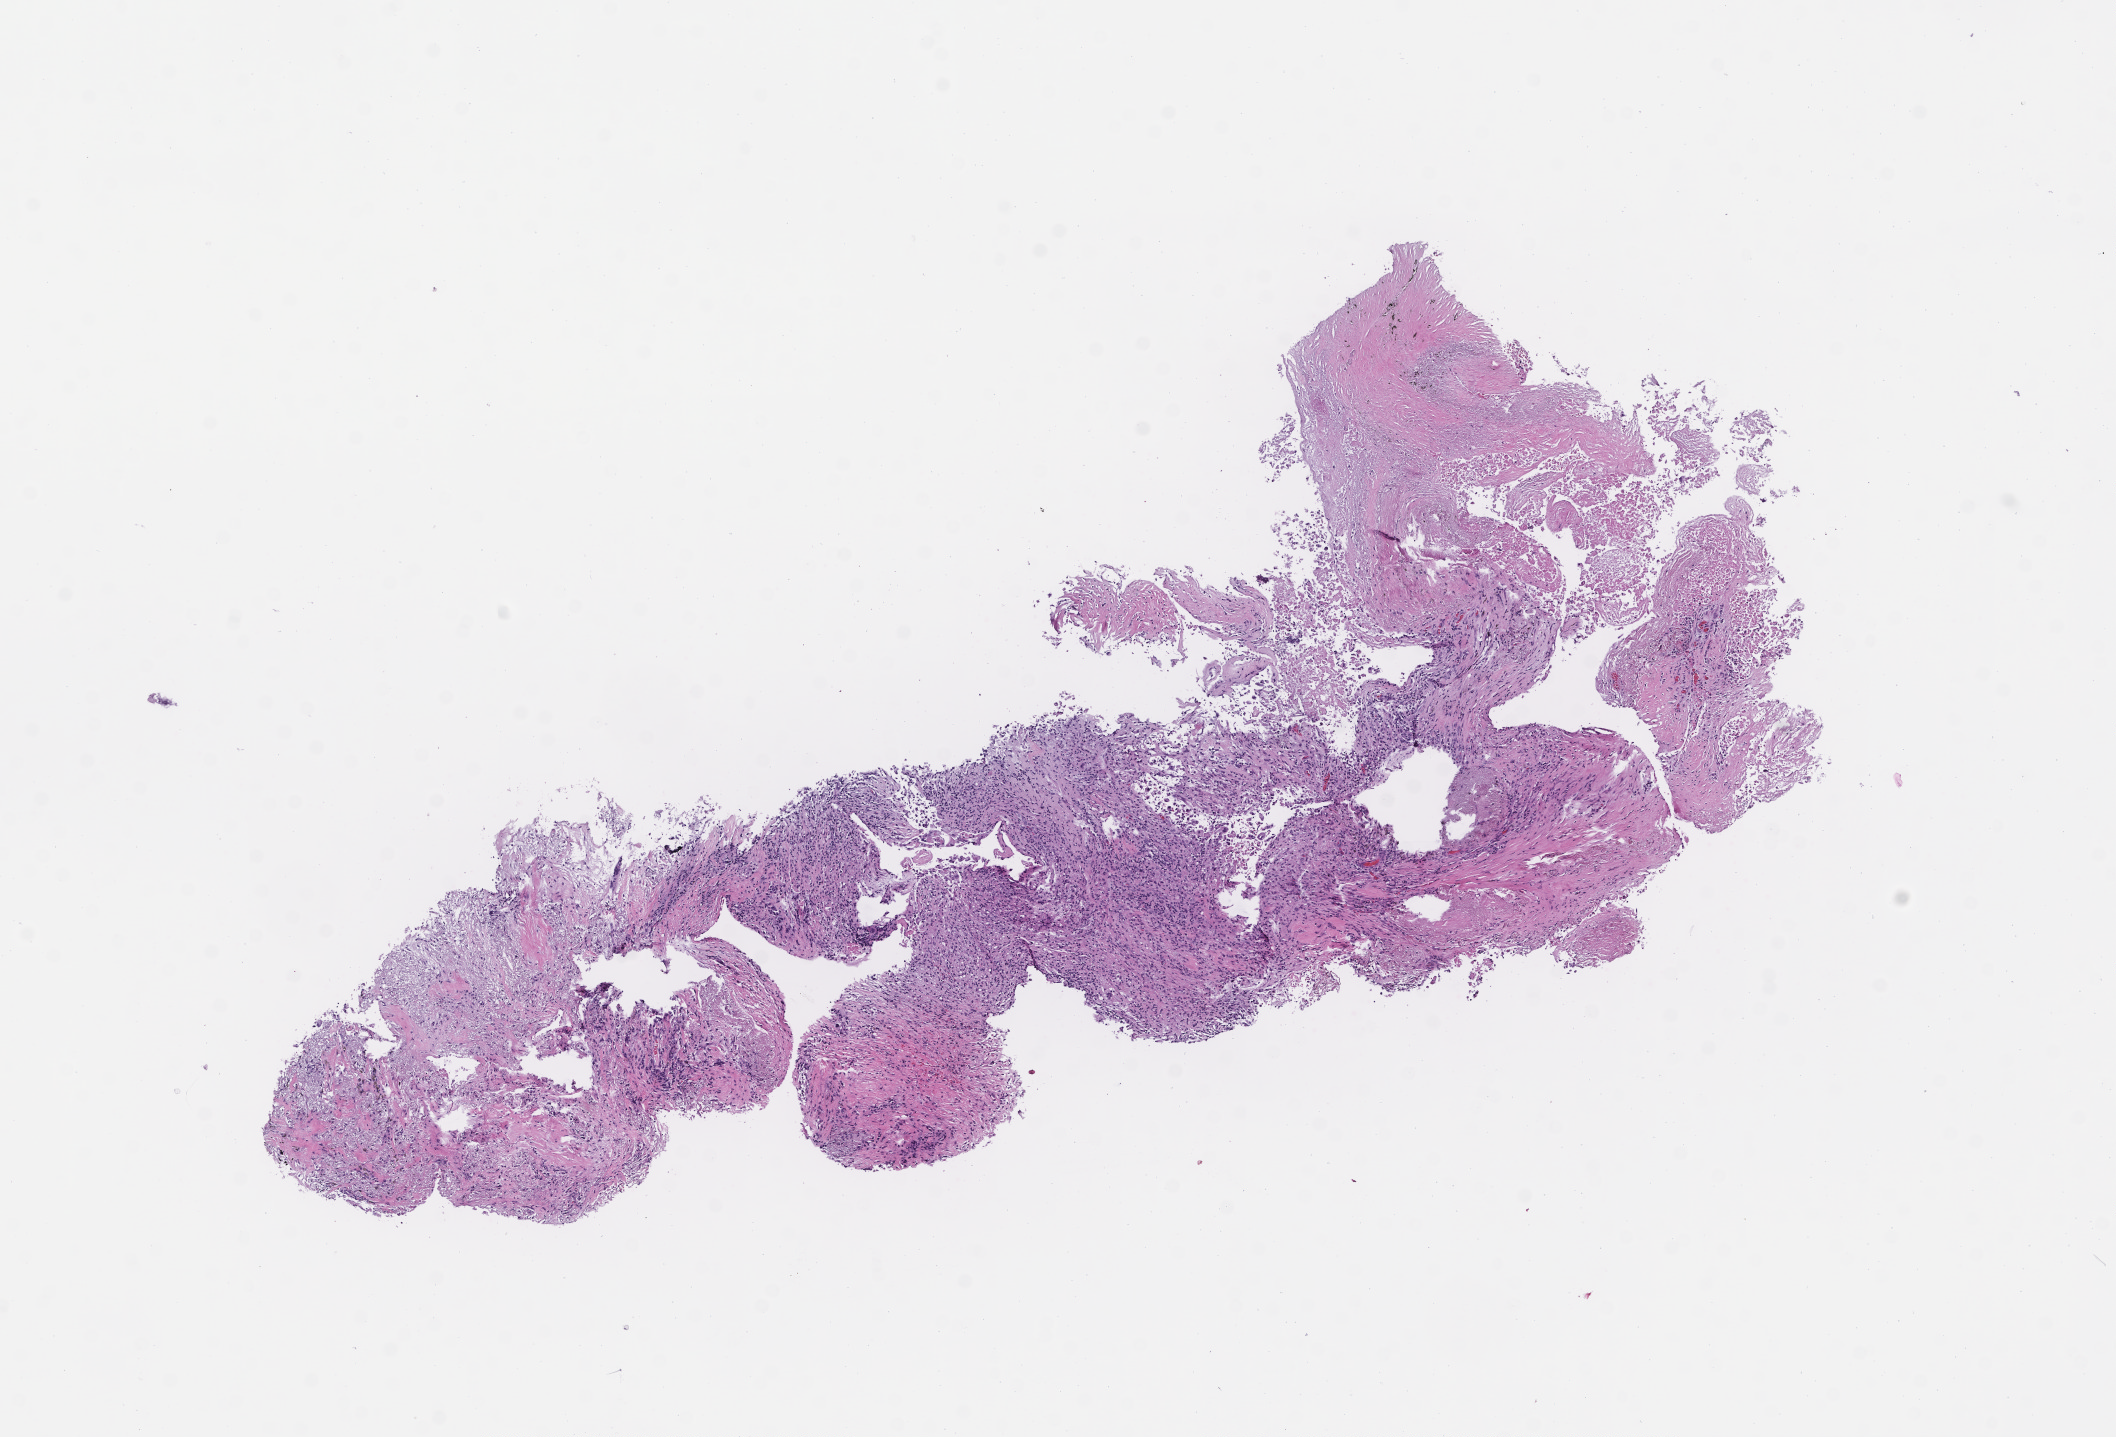
Haematoxylin and eosin whole-slide image, a low-resolution overview of the entire scanned area, about 8.5 x 5.8 mm. Formalin-fixed, paraffin-embedded (FFPE) tissue. Tissue site: lung. Collected at baseline (before treatment). Male patient.
This section: primary tumor. Diagnosis: Non-Small Cell Lung Carcinoma.